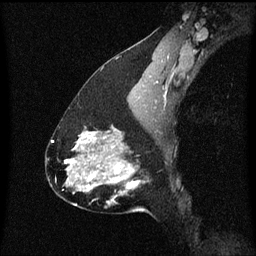
Breast MRI (dynamic contrast-enhanced), one sagittal slice; slice 37 of 60 in the series (ordered by position); dynamic contrast-enhanced series, image 2 of 3 at this slice position (ordered by acquisition); 1.5 T; TE 4.2 ms, TR 8.4 ms; 2 mm slice thickness; 256 × 256 image matrix, field of view 200 × 200 mm. Female patient, age 47 years.
Outlined on this slice (semi-automatically segmented with operator editing):
- analysis volume of interest (the breast-tissue region the enhancement analysis was run in; not a lesion): bounding box <81,138,151,215> (left, top, right, bottom; pixels)
- tumour enhancement mask (voxels above the 70 % enhancement threshold inside the analysis volume of interest): <81,138,139,203>